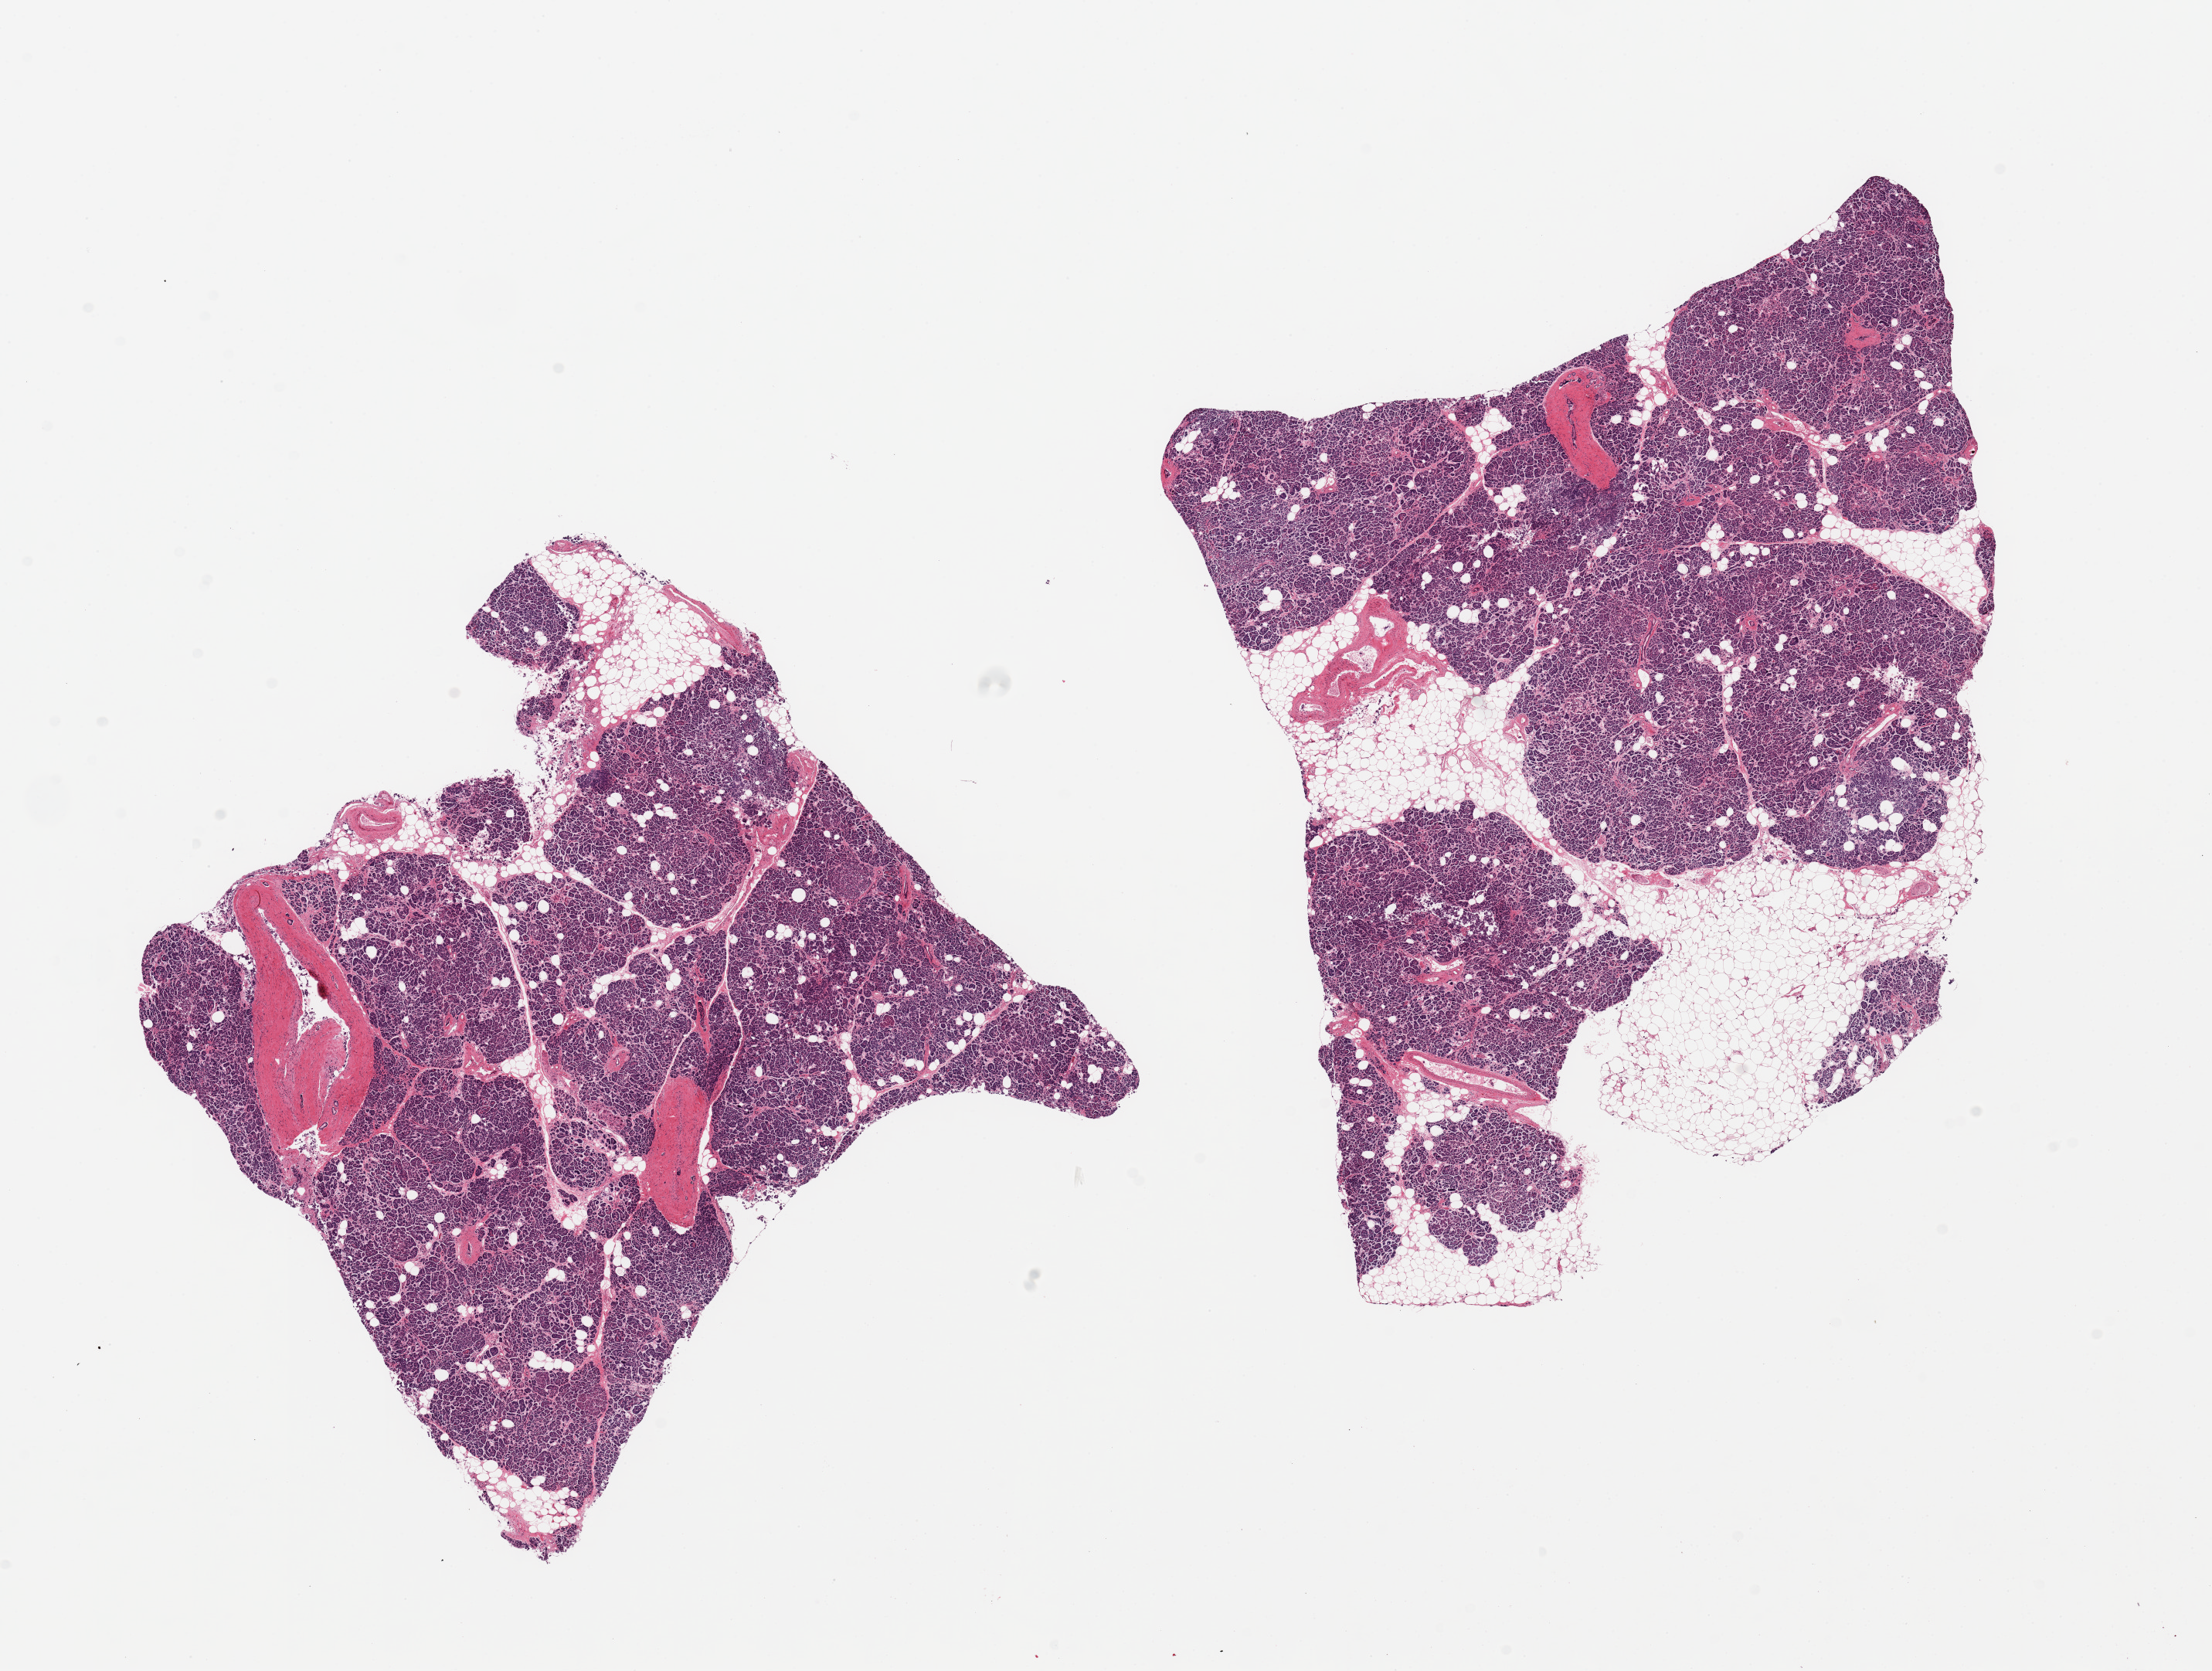
Whole-slide image, hematoxylin and eosin (H&E) stain, a low-resolution overview of the entire scanned area, about 22.6 x 17.1 mm (slide scanned at 20x). PAXgene-fixed, paraffin-embedded tissue. Sampled site (target tissue): pancreas. Donor tissue sample. Male donor.
Pathologist's review note for this sample: 2 pieces; includes 10 and 30% fat, some intraacinar fibrosis, islets well visualized.